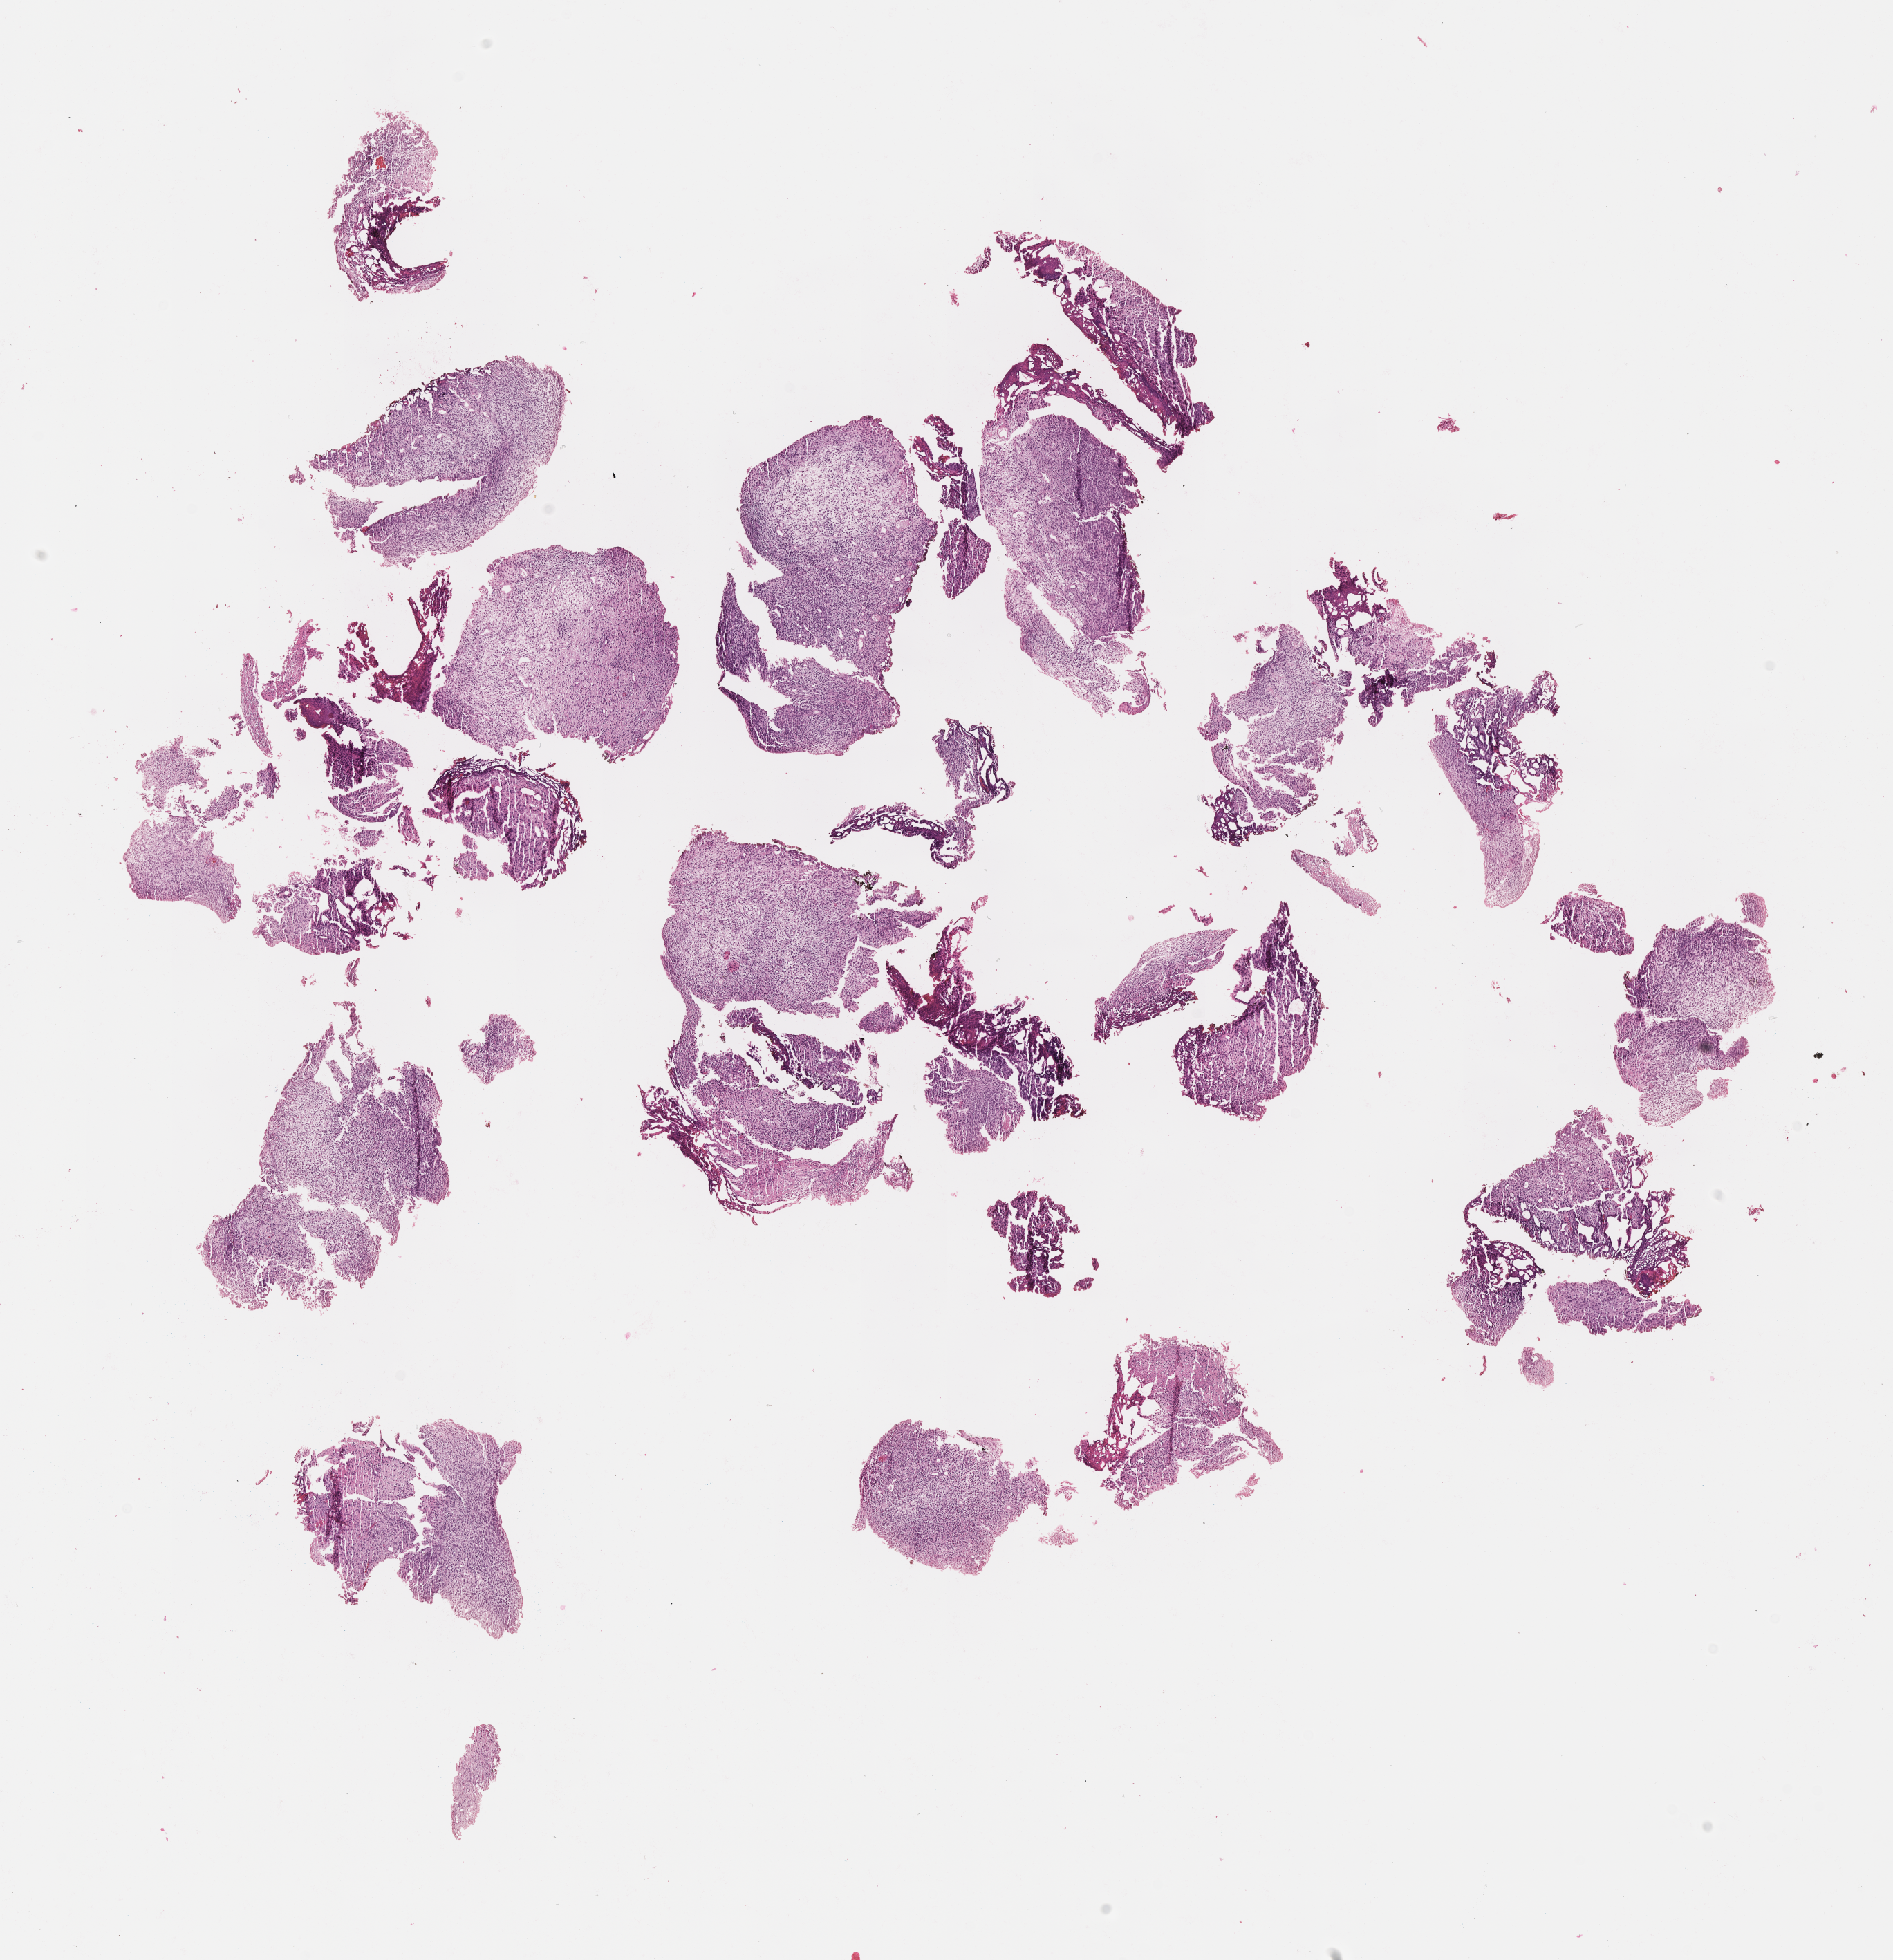
Haematoxylin and eosin whole-slide image of tumor tissue, a low-resolution overview of the entire scanned area, about 11.1 x 11.5 mm, FFPE section, site: prostate. Patient: male, age 1.9 years at diagnosis.
Diagnosis: rhabdomyosarcoma; histological classification: embryonal rhabdomyosarcoma.